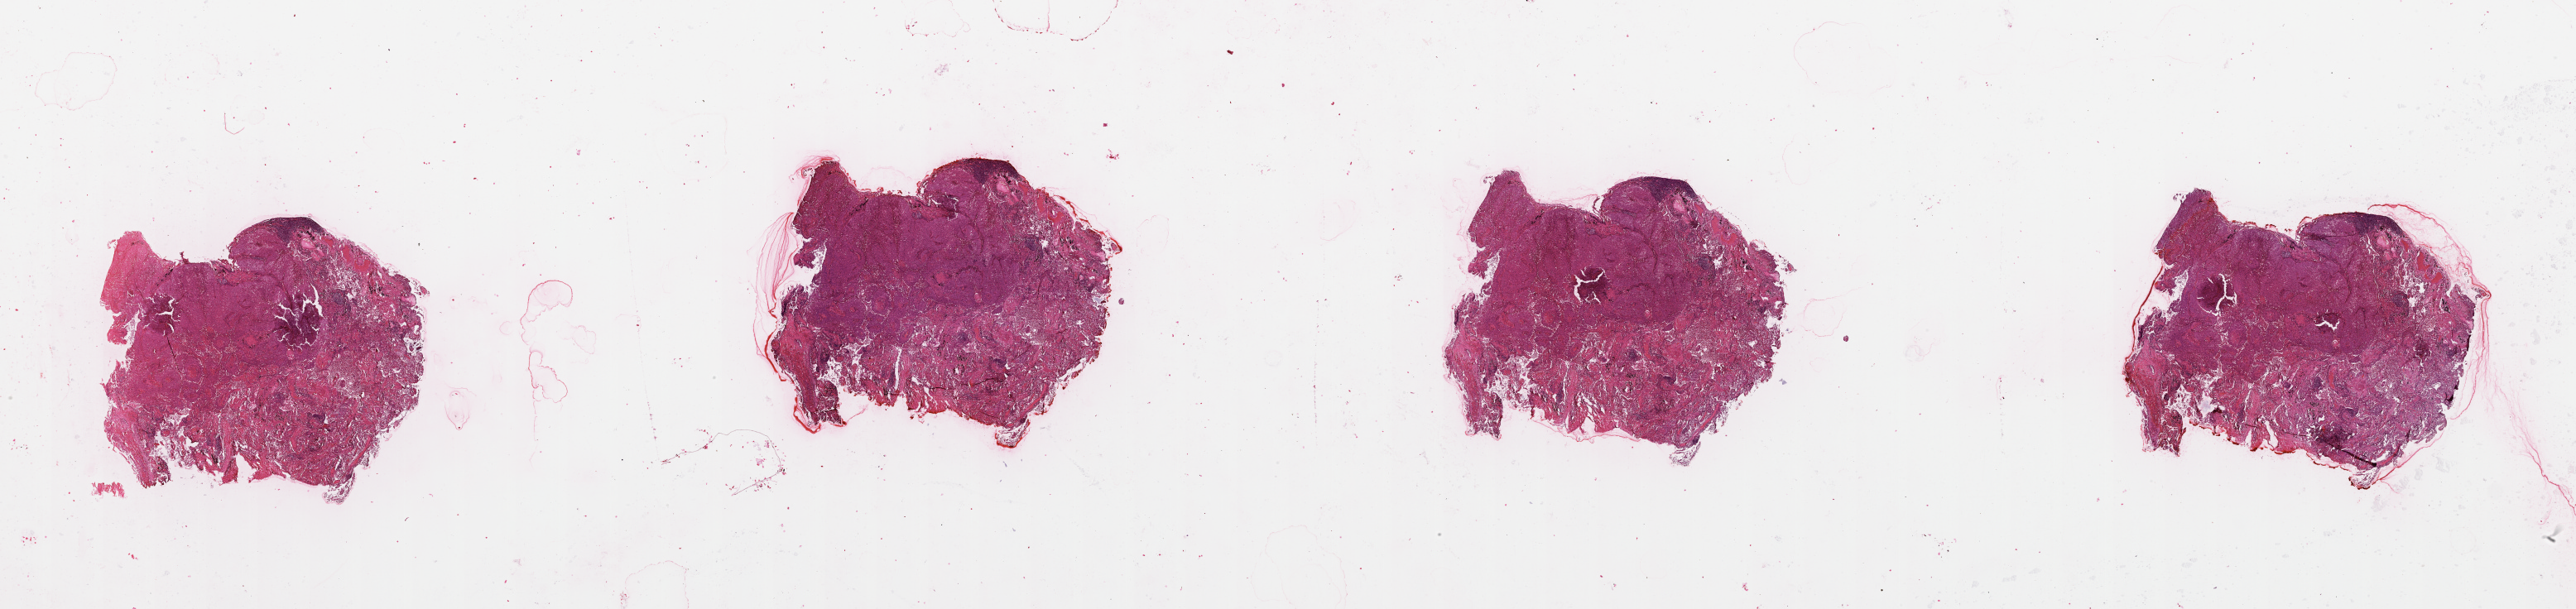
Whole-slide histology image, H&E, low-resolution overview of the scanned area, about 50.1 x 11.9 mm (slide scanned at 20x); lung, tissue type not recorded.
Patient diagnosis (cohort enrolment): squamous cell carcinoma (lung).